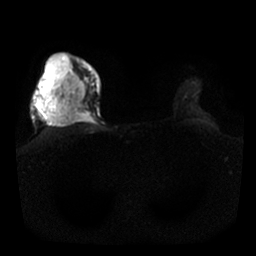
Breast MRI, one axial slice. Position 21 of 25 along the scan axis. Diffusion-weighted series; image 2 of 4 stored at this slice position (different b-values; order by instance number). 1.5 T. 4 mm slice thickness. 256 × 256 image matrix, field of view 340 × 340 mm. Female patient.
Outlined on this slice (expert manual segmentation):
- tumour on diffusion-weighted imaging: box from (x=38, y=52) to (x=91, y=125) px